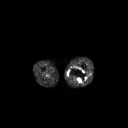
FDG PET of an extremity soft-tissue mass (from a PET/CT study), one axial slice. Position 220 of 267 along the scan axis. 3.27 mm slice thickness. 128 × 128 image matrix. Patient: male, 44 years. From the clinical record (not read from this slice): histological type: undifferentiated pleomorphic liposarcoma; grade: high; site of the primary tumour: left thigh.
Structures marked on this image (expert contour drawn on MRI and transferred to this co-registered scan by the dataset authors):
- gross tumour volume including surrounding oedema: box from (x=68, y=67) to (x=87, y=83) px
- gross tumour volume (mass): (x=68, y=67)–(x=87, y=83)